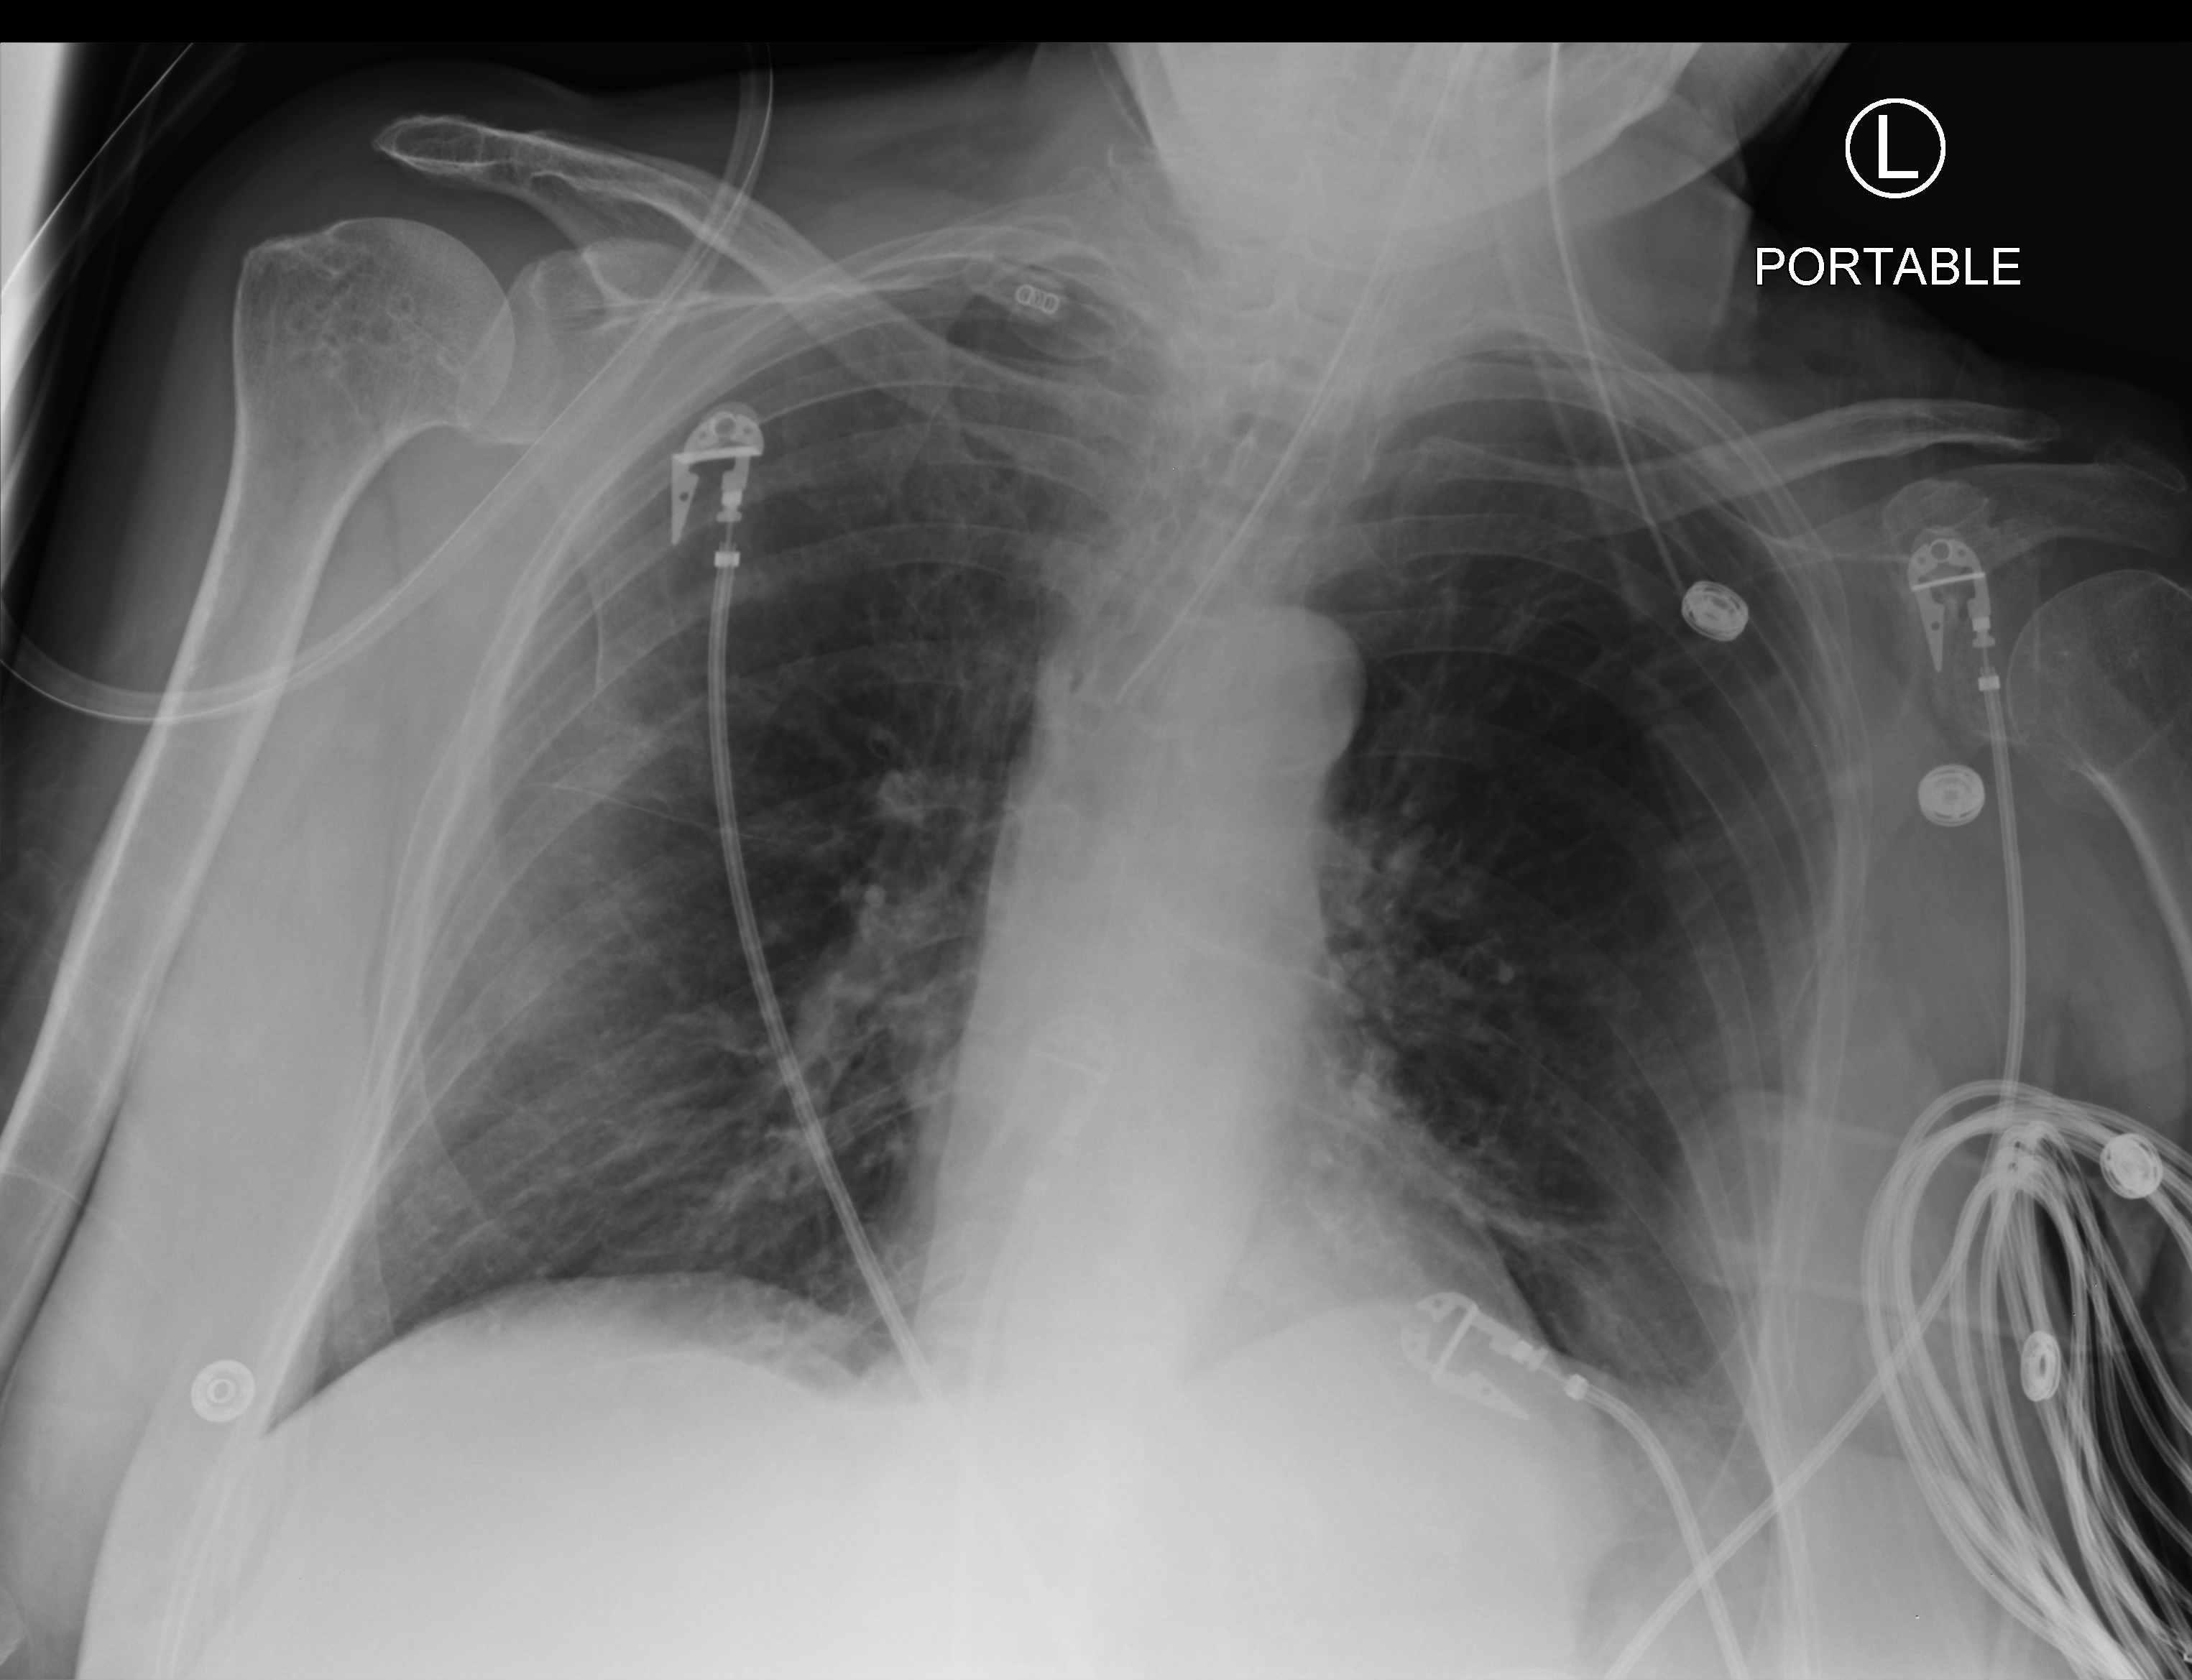
Portable chest radiograph; anteroposterior (AP) projection. Patient hospitalised with COVID-19; female, aged 75–90 years.
Admission-level facts for this patient (not findings on this image; timing relative to this image not recorded): mechanically ventilated during this hospital stay: yes.